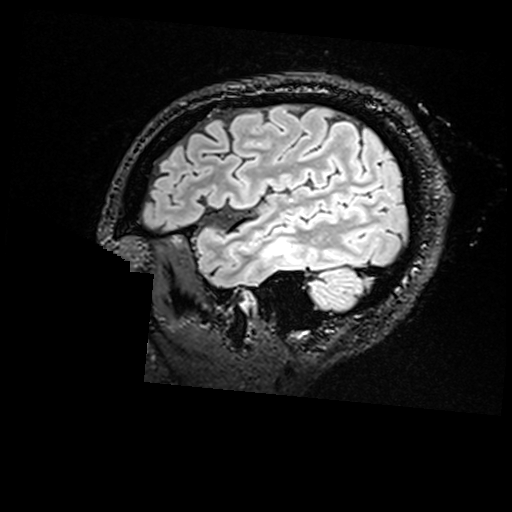
Brain MRI from a brain-tumour surgery series, one sagittal slice. Slice 130 of 176 in the series (ordered by position). T2 FLAIR. 1 mm slice thickness. 512 × 512 image matrix, field of view 250 × 250 mm. From the clinical record (not read from this slice): histopathology: Non-tumor destructive chronic inflammatory lesion with abnormal vasculature; tumour location: Right Inferior Temporal.
Outlined on this slice (expert manual segmentation):
- residual tumour: bounding box (x1, y1, x2, y2) in pixels: (284, 244, 289, 251)